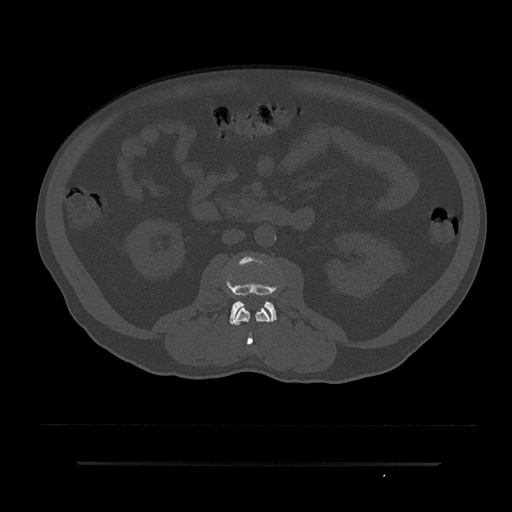
CT including the spine, one axial slice. Slice 36 of 797 in the series (ordered by position). Reconstruction kernel Br40s/3. 120 kVp. Bone window (W 1800 / L 400 HU). 0.5 mm slice thickness. 512 × 512 image matrix, field of view 464 × 464 mm. Male patient, age 59 years. Case-level facts recorded for this patient, not image findings: primary cancer: bile ducts; vertebrae with lytic lesions (as recorded): T10.
Outlined on this slice (semi-automatic segmentation, software-assisted and operator-edited):
- L2 vertebra: box from (x=233, y=306) to (x=272, y=346) px
- L3 vertebra: (x=228, y=257)–(x=276, y=325)